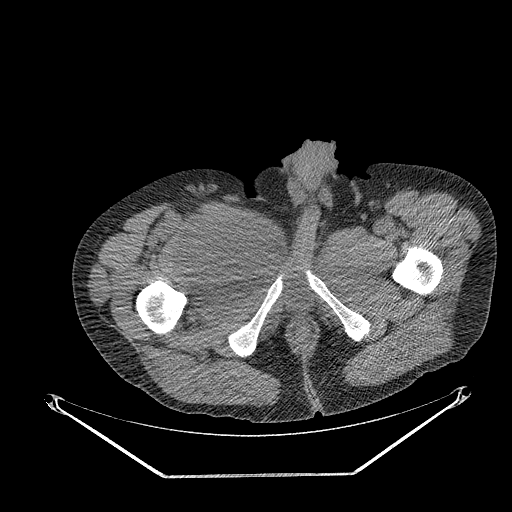
CT of an extremity soft-tissue mass (from a PET/CT study), one axial slice; position 287 of 311 along the scan axis; reconstruction kernel STANDARD; 140 kVp; soft-tissue window (W 400 / L 40 HU); 3.75 mm slice thickness; 512 × 512 image matrix. Male patient. Case-level facts recorded for this patient, not image findings: histological type: undifferentiated - pleiomorphic; grade: high; site of the primary tumour: right thigh.
Annotated regions visible in this slice (expert contour drawn on MRI and transferred to this co-registered scan by the dataset authors):
- gross tumour volume including surrounding oedema: bounding box <199,208,257,268> (left, top, right, bottom; pixels)
- gross tumour volume (mass): <199,215,250,263>